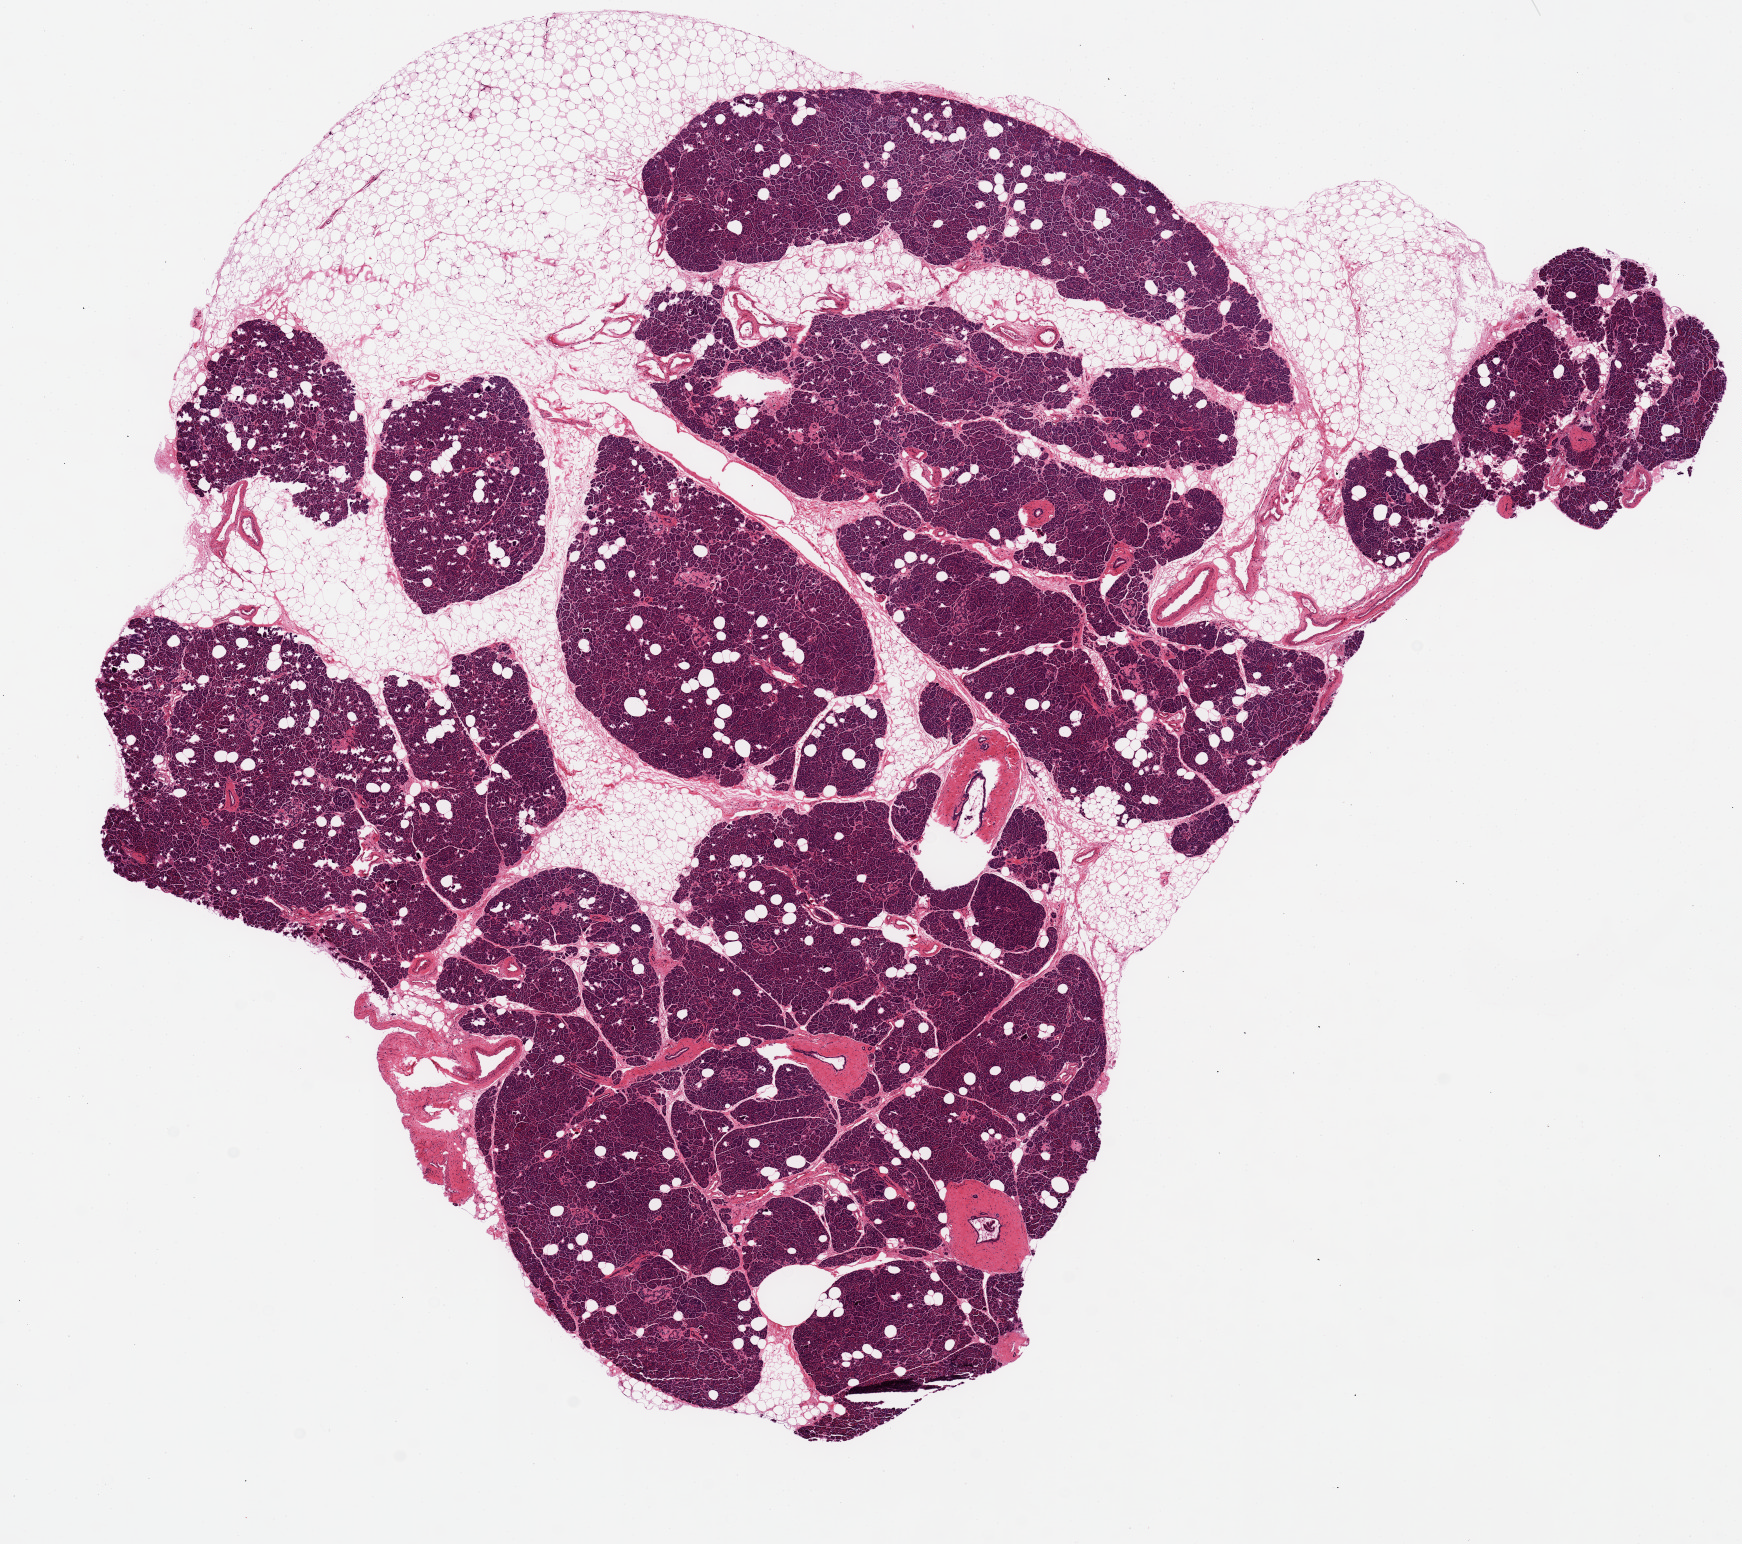
Whole-slide image, haematoxylin and eosin stain, brightfield — whole scanned area (about 13.8 x 12.2 mm, from a 20x scan) shown as a low-resolution overview, PAXgene-fixed, paraffin-embedded tissue, target tissue: pancreas, donor tissue sample. Male donor.
Review note (as recorded): Remarkably well preserved. Mild focal saponifcation. Parenchyma is about 70% of specimen.